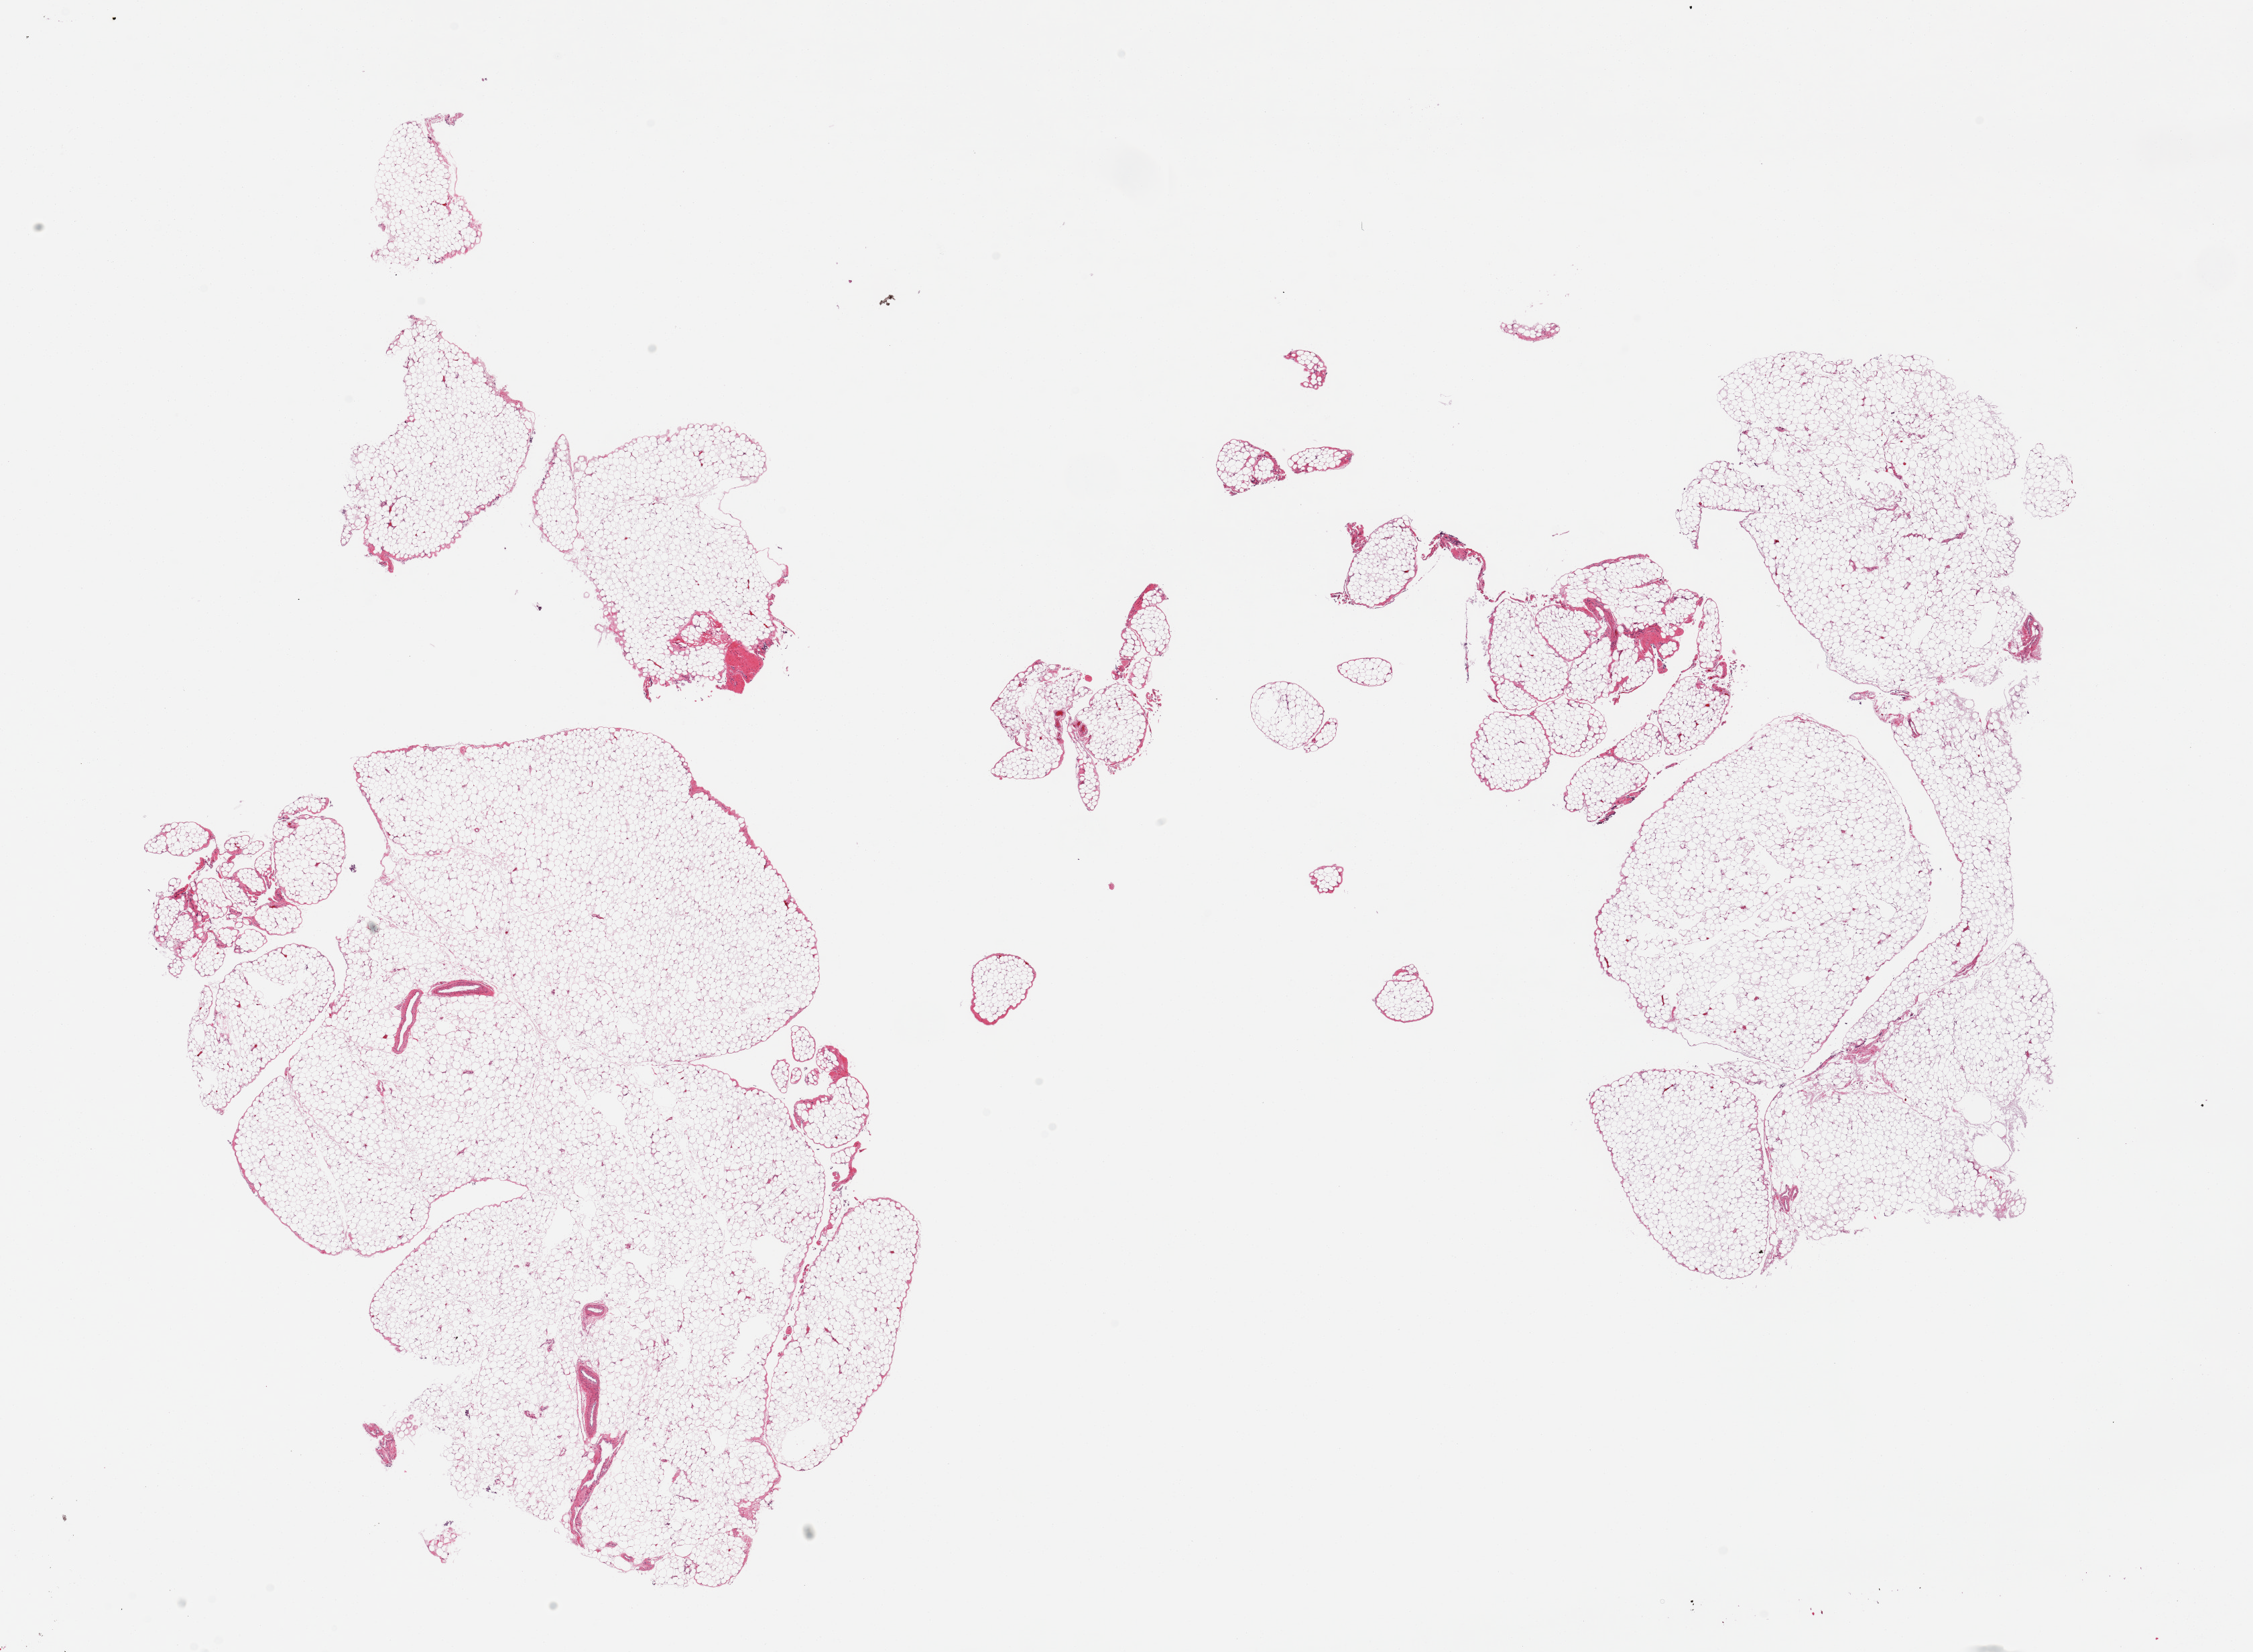
Whole-slide image, H&E stain, brightfield — low-resolution overview of the scanned area, about 26.6 x 19.5 mm, PAXgene-fixed, paraffin-embedded tissue, section of omentum (target tissue), donor tissue sample. Donor: male.
* reviewer comment on this tissue sample: 2 pieces, minimal fascia